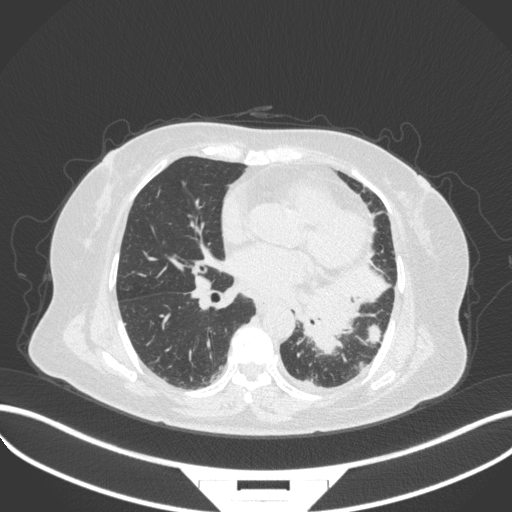
Chest CT, one axial slice. Reconstruction kernel B31f. 120 kVp. Lung window (W 1500 / L -600 HU). 512 × 512 image matrix, field of view 400 × 400 mm. Female patient, age 69 years. Case-level facts recorded for this patient, not image findings: clinical TNM (as recorded): T2b N3 M1.
Structures marked on this image (bounding box drawn by a radiologist):
- lung tumour (recorded histology: adenocarcinoma): bounding box [x1, y1, x2, y2] px = [298, 279, 365, 355]